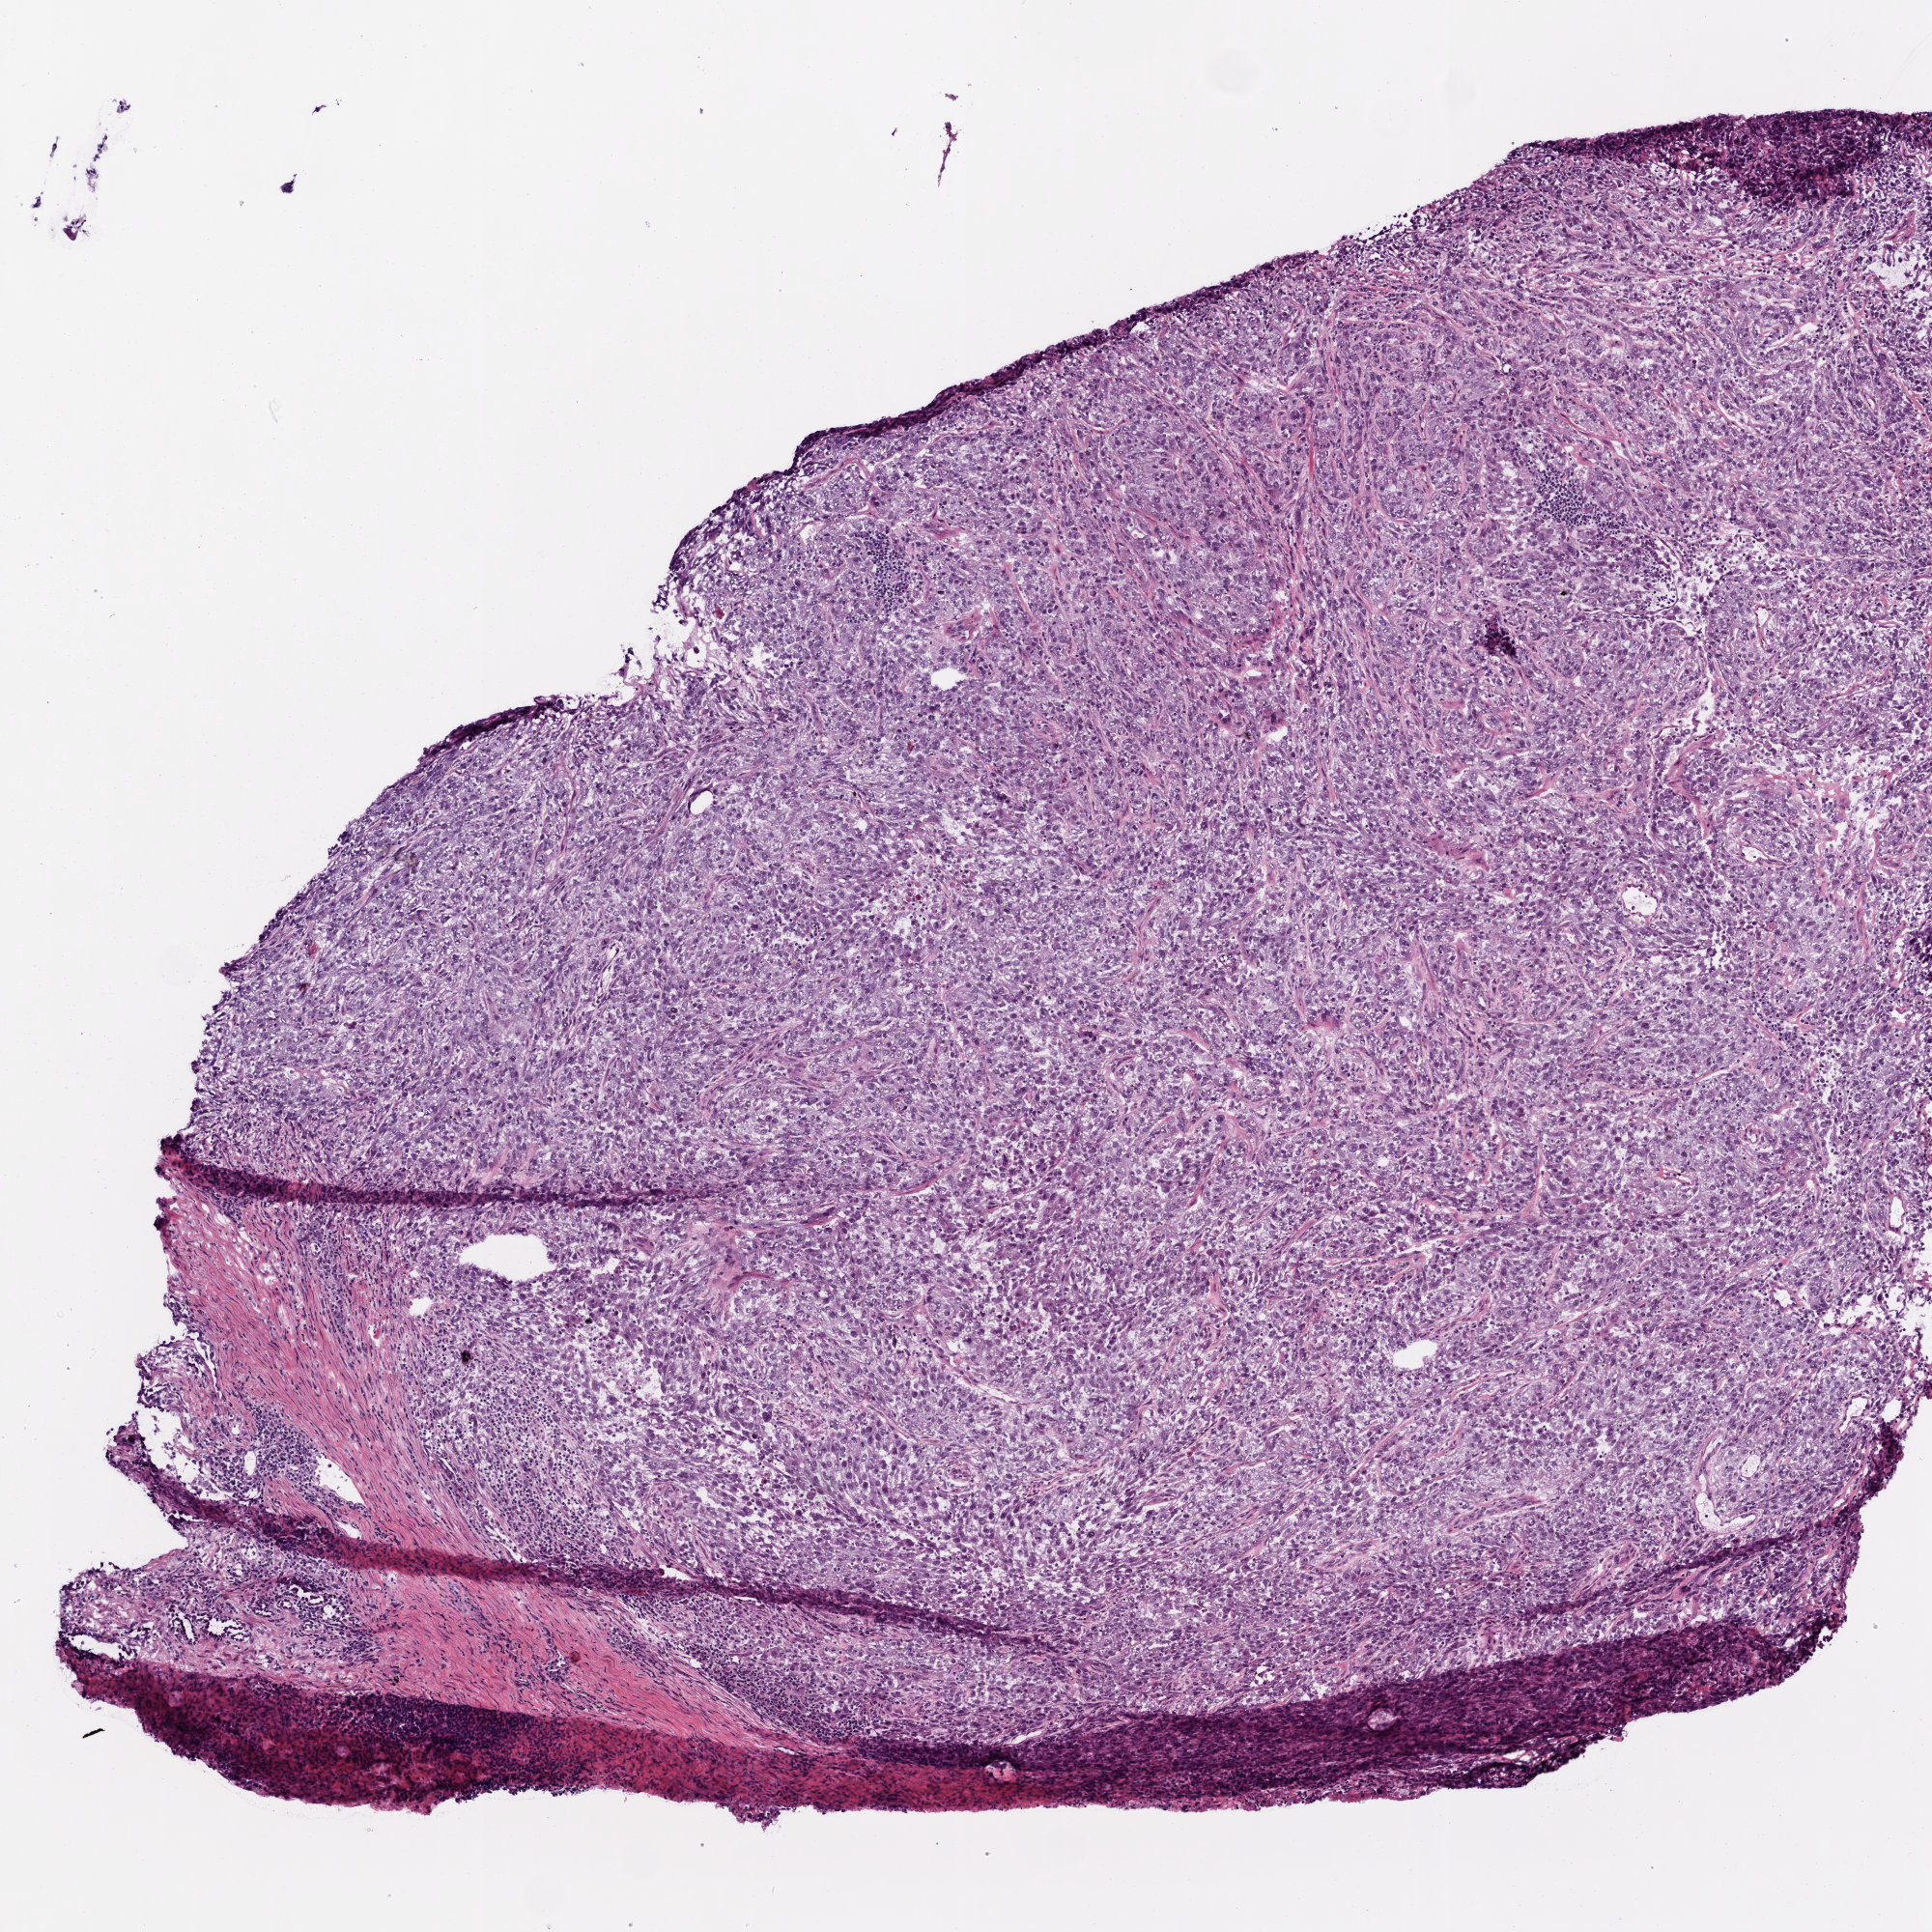
Digitized H&E-stained tissue section (whole slide), shown as a low-resolution overview of the whole scanned area (about 4.0 x 4.0 mm, acquisition: 20x scan), frozen section from the top of the tissue portion, primary tumour sample from the lung. Female patient; age at initial diagnosis 66 years. Pathologist review of this section (percent, as recorded): tumour cells 92%, tumour nuclei 85%, normal cells 2%, stromal cells 2%, necrosis 2%.
AJCC pathologic stage: IB (5th edition). TNM: T2a N0 M0. Pathologic diagnosis: Adenocarcinoma, NOS (upper lobe, lung).